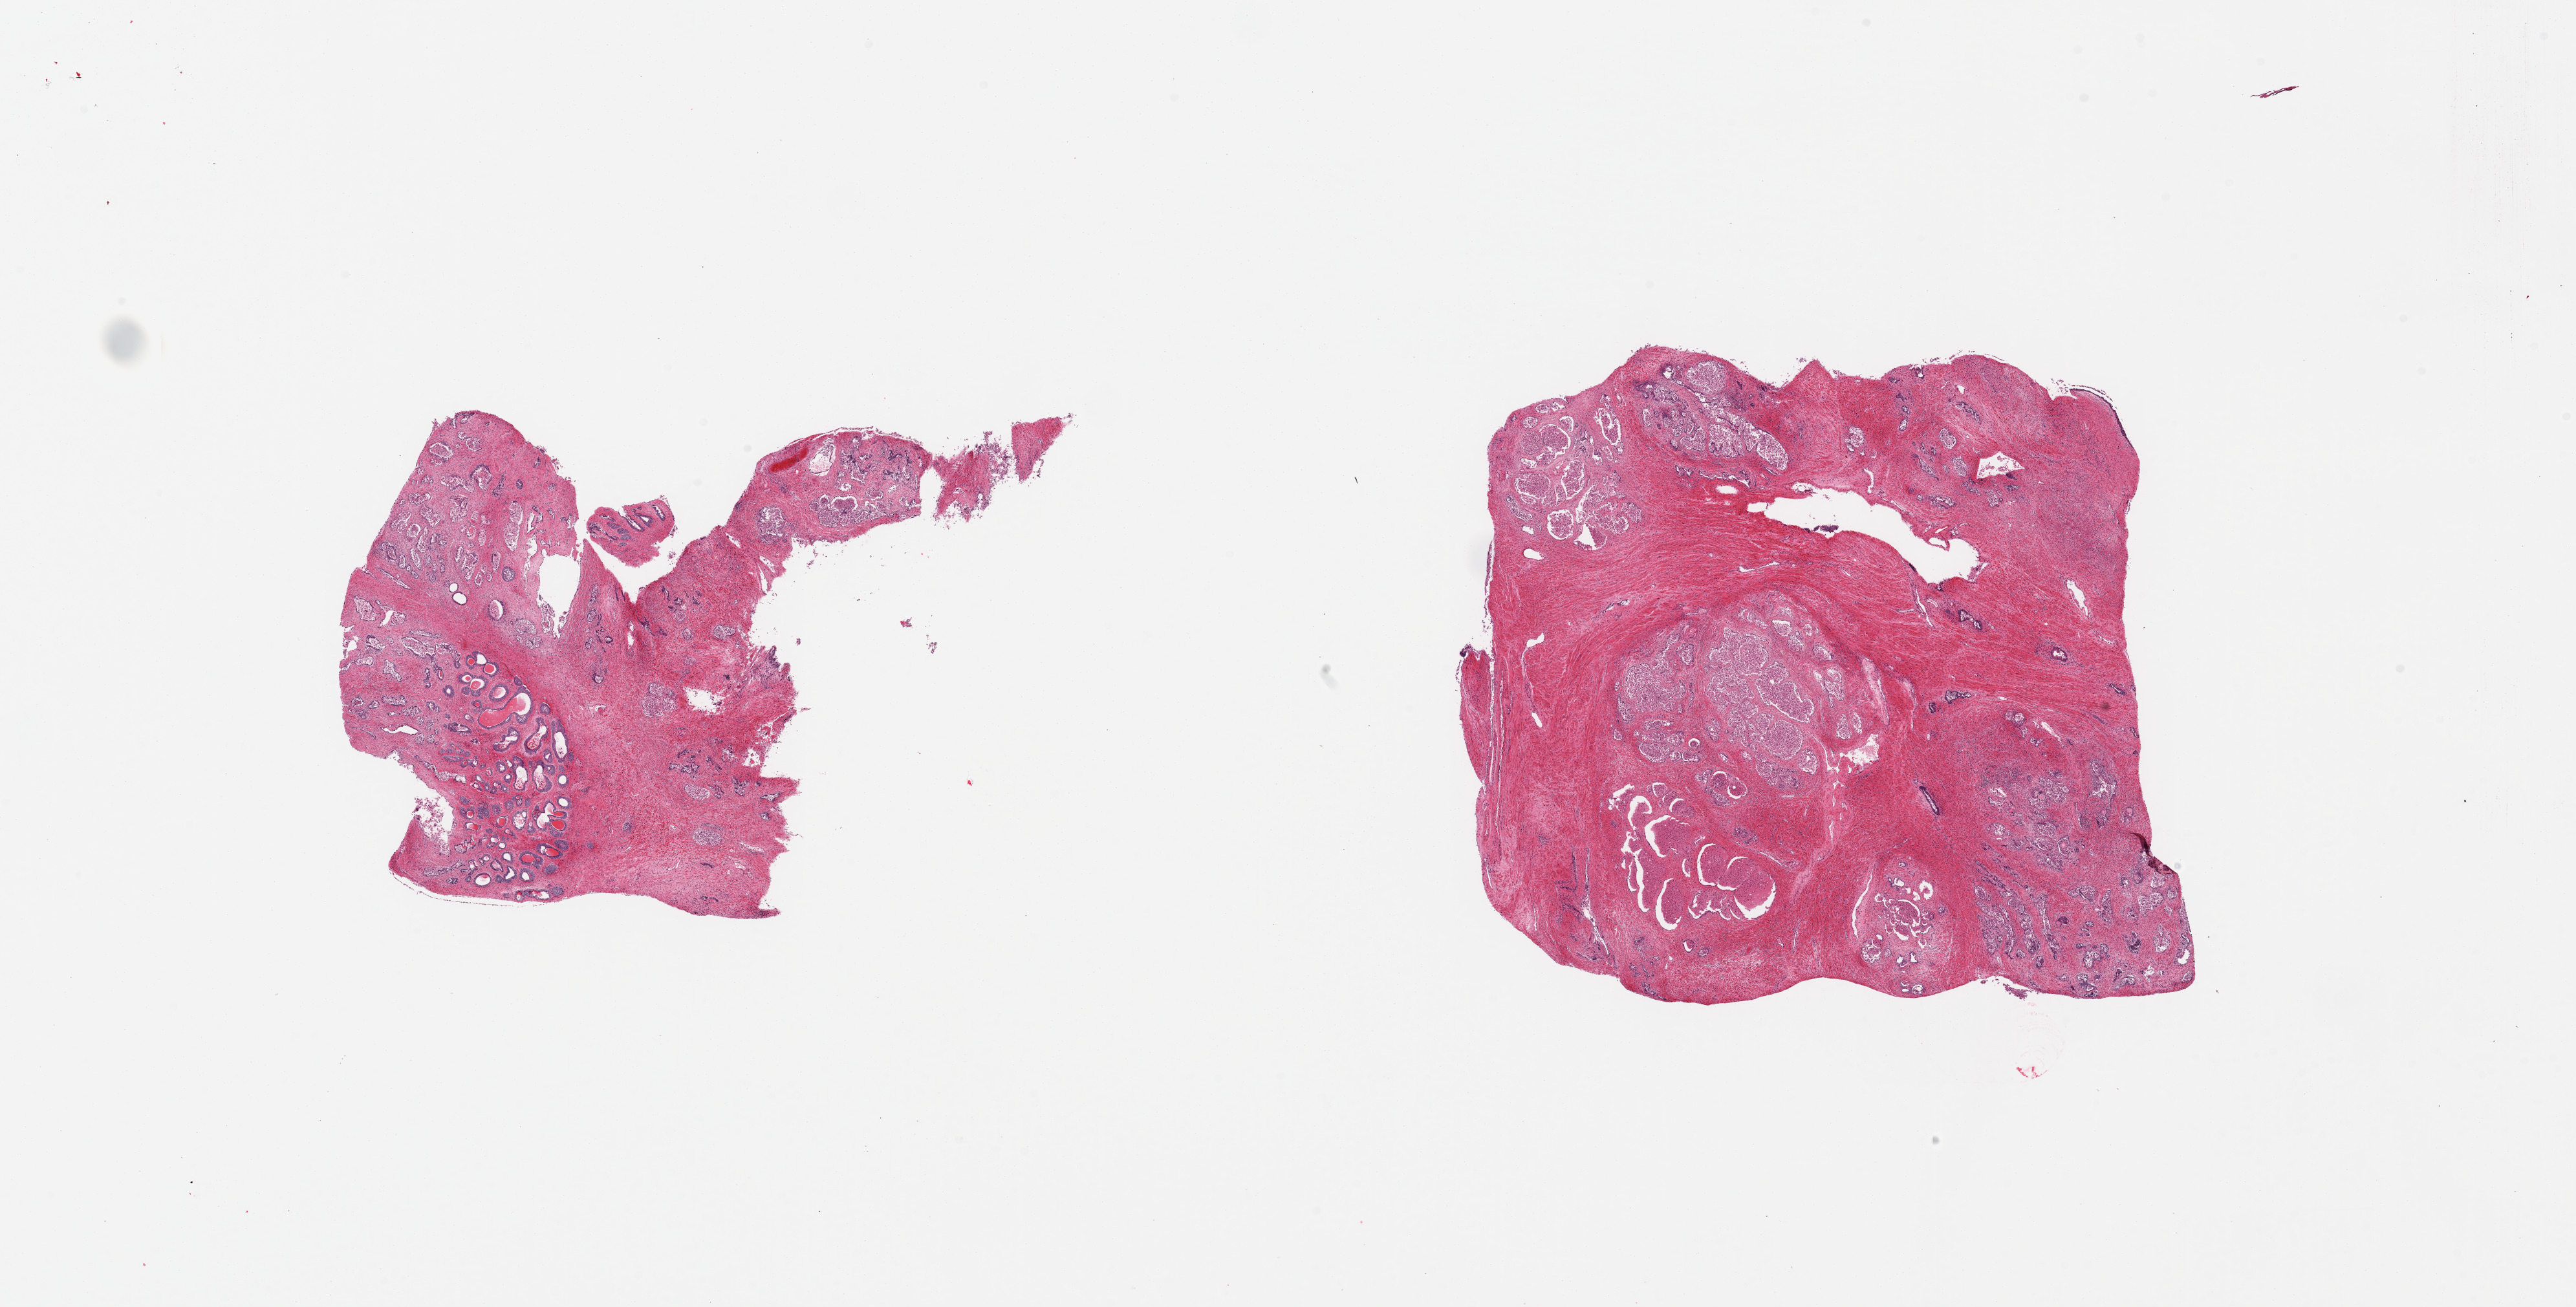
Haematoxylin and eosin whole-slide image, low-resolution overview of the scanned area, about 31.5 x 16.0 mm (from a 20x scan). PAXgene-fixed, paraffin-embedded tissue. Section of prostate (target tissue). Tissue donor sample.
Review note (as recorded): 2 pieces; fibromuscular stroma with multinodular parenchyma; glands severely autolyzed, epithelial hyperplasia.